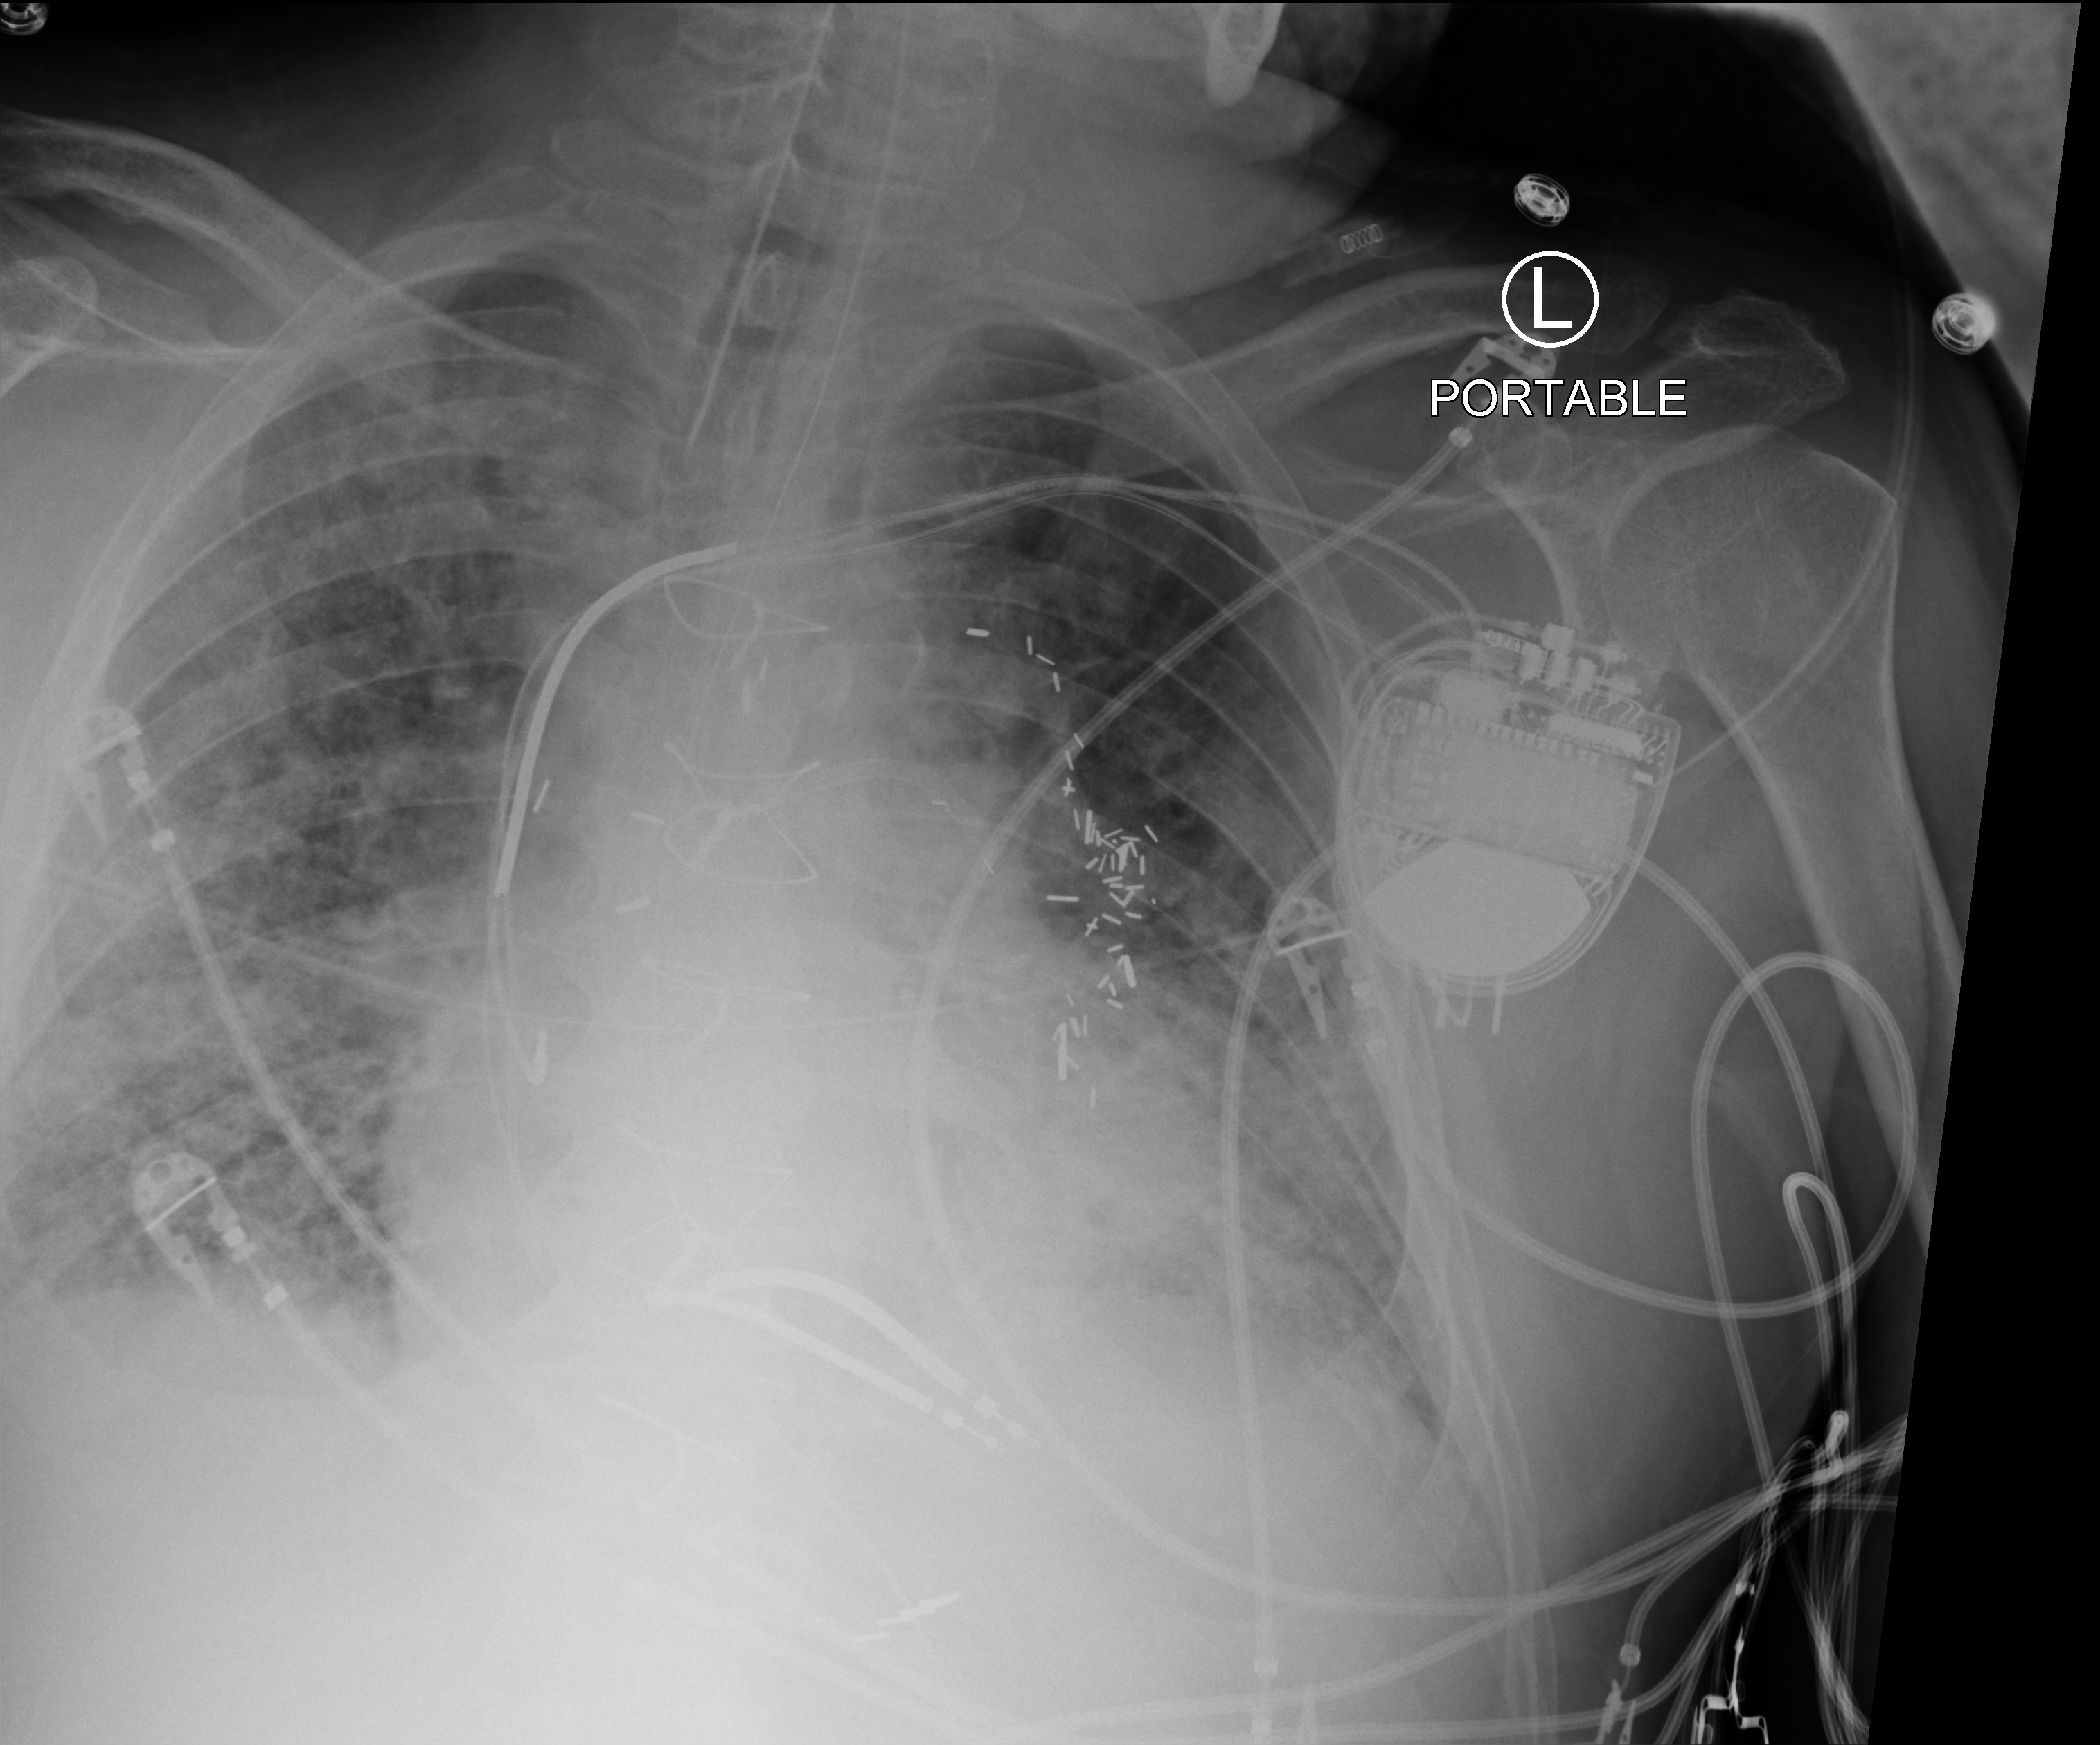
Chest X-ray (portable), anteroposterior (AP) projection. Patient hospitalised with COVID-19; male, aged 60–74 years.
Hospital-stay facts (about this admission, not read from this image; timing relative to this image not recorded):
- admitted to intensive care during this hospital stay: yes